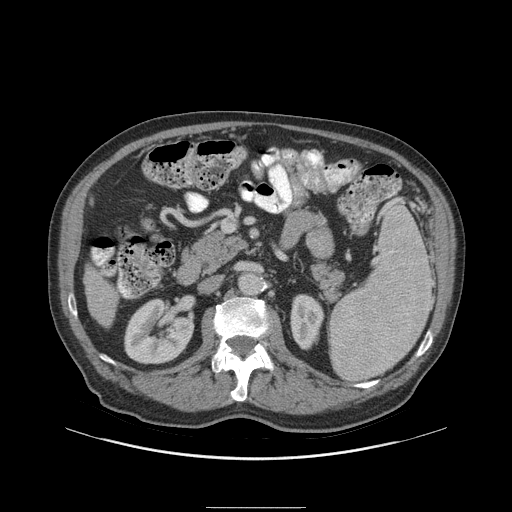
Contrast-enhanced abdominal CT (liver protocol), one axial slice; reconstruction kernel STANDARD; 140 kVp; soft-tissue window (W 400 / L 40 HU); 2.5 mm slice thickness; 512 × 512 image matrix, field of view 440 × 440 mm. Case-level facts recorded for this patient, not image findings: diagnosis: hepatocellular carcinoma (patient treated with transarterial chemoembolisation; whether this scan precedes or follows treatment is not stated here); TNM stage (as recorded): Stage-I; Child-Pugh class: A; tumour nodularity: uninodular; tumour size: 5.1 cm.
Annotated regions visible in this slice (semi-automatic segmentation, software-assisted and operator-edited):
- liver parenchyma outside the tumour (the mass and vessels are separate outlines, so this box may not span the whole liver): box from (x=84, y=264) to (x=118, y=327) px